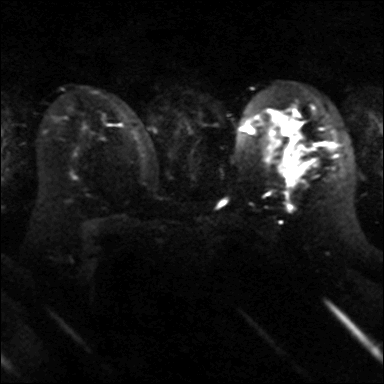
Breast MRI, one axial slice; diffusion-weighted series; image 2 of 4 stored at this slice position (different b-values; order by instance number); 3 T; 4 mm slice thickness; 384 × 384 image matrix, field of view 320 × 320 mm. Female patient.
Outlined on this slice (outlined manually by an expert reader):
- tumour on diffusion-weighted imaging: box from (x=300, y=147) to (x=309, y=155) px